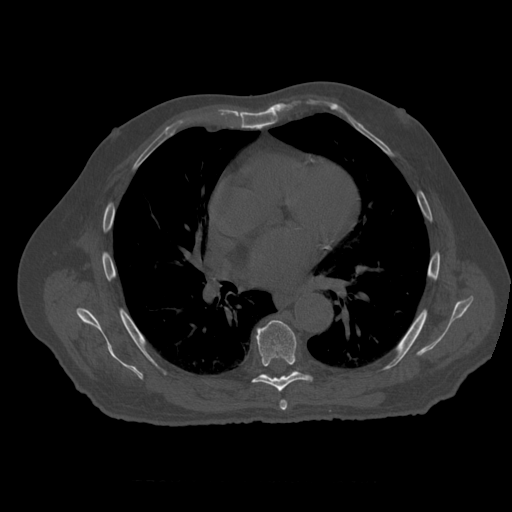
CT including the spine, one axial slice; position 362 of 399 along the scan axis; reconstruction kernel STANDARD; bone window (W 1800 / L 400 HU); 1.25 mm slice thickness; 512 × 512 image matrix. Patient age 73 years. From the clinical record (not read from this slice): primary cancer: prostate.
Structures marked on this image (semi-automatically segmented with operator editing):
- T6 vertebra: bounding box (x1, y1, x2, y2) in pixels: (280, 400, 288, 411)
- T7 vertebra: (253, 321, 311, 392)